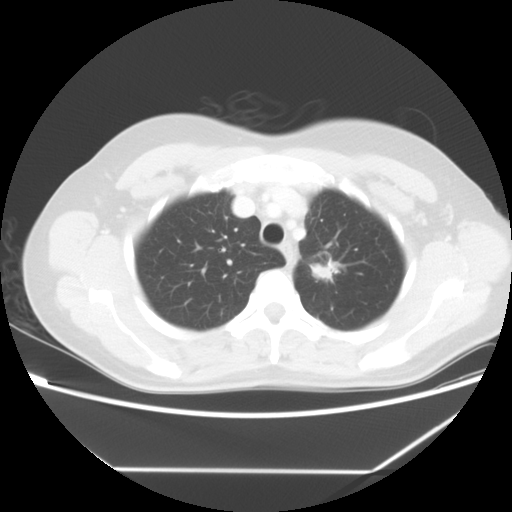
Chest CT, one axial slice; position 47 of 60 along the scan axis; lung window (W 1500 / L -600 HU); 5 mm slice thickness; 512 × 512 image matrix, field of view 367 × 367 mm. Patient: female, 43 years. Case-level facts recorded for this patient, not image findings: clinical TNM (as recorded): T1c N0 M1b.
Structures marked on this image (bounding box drawn by a radiologist):
- lung tumour (recorded histology: adenocarcinoma): box from (x=307, y=258) to (x=345, y=282) px